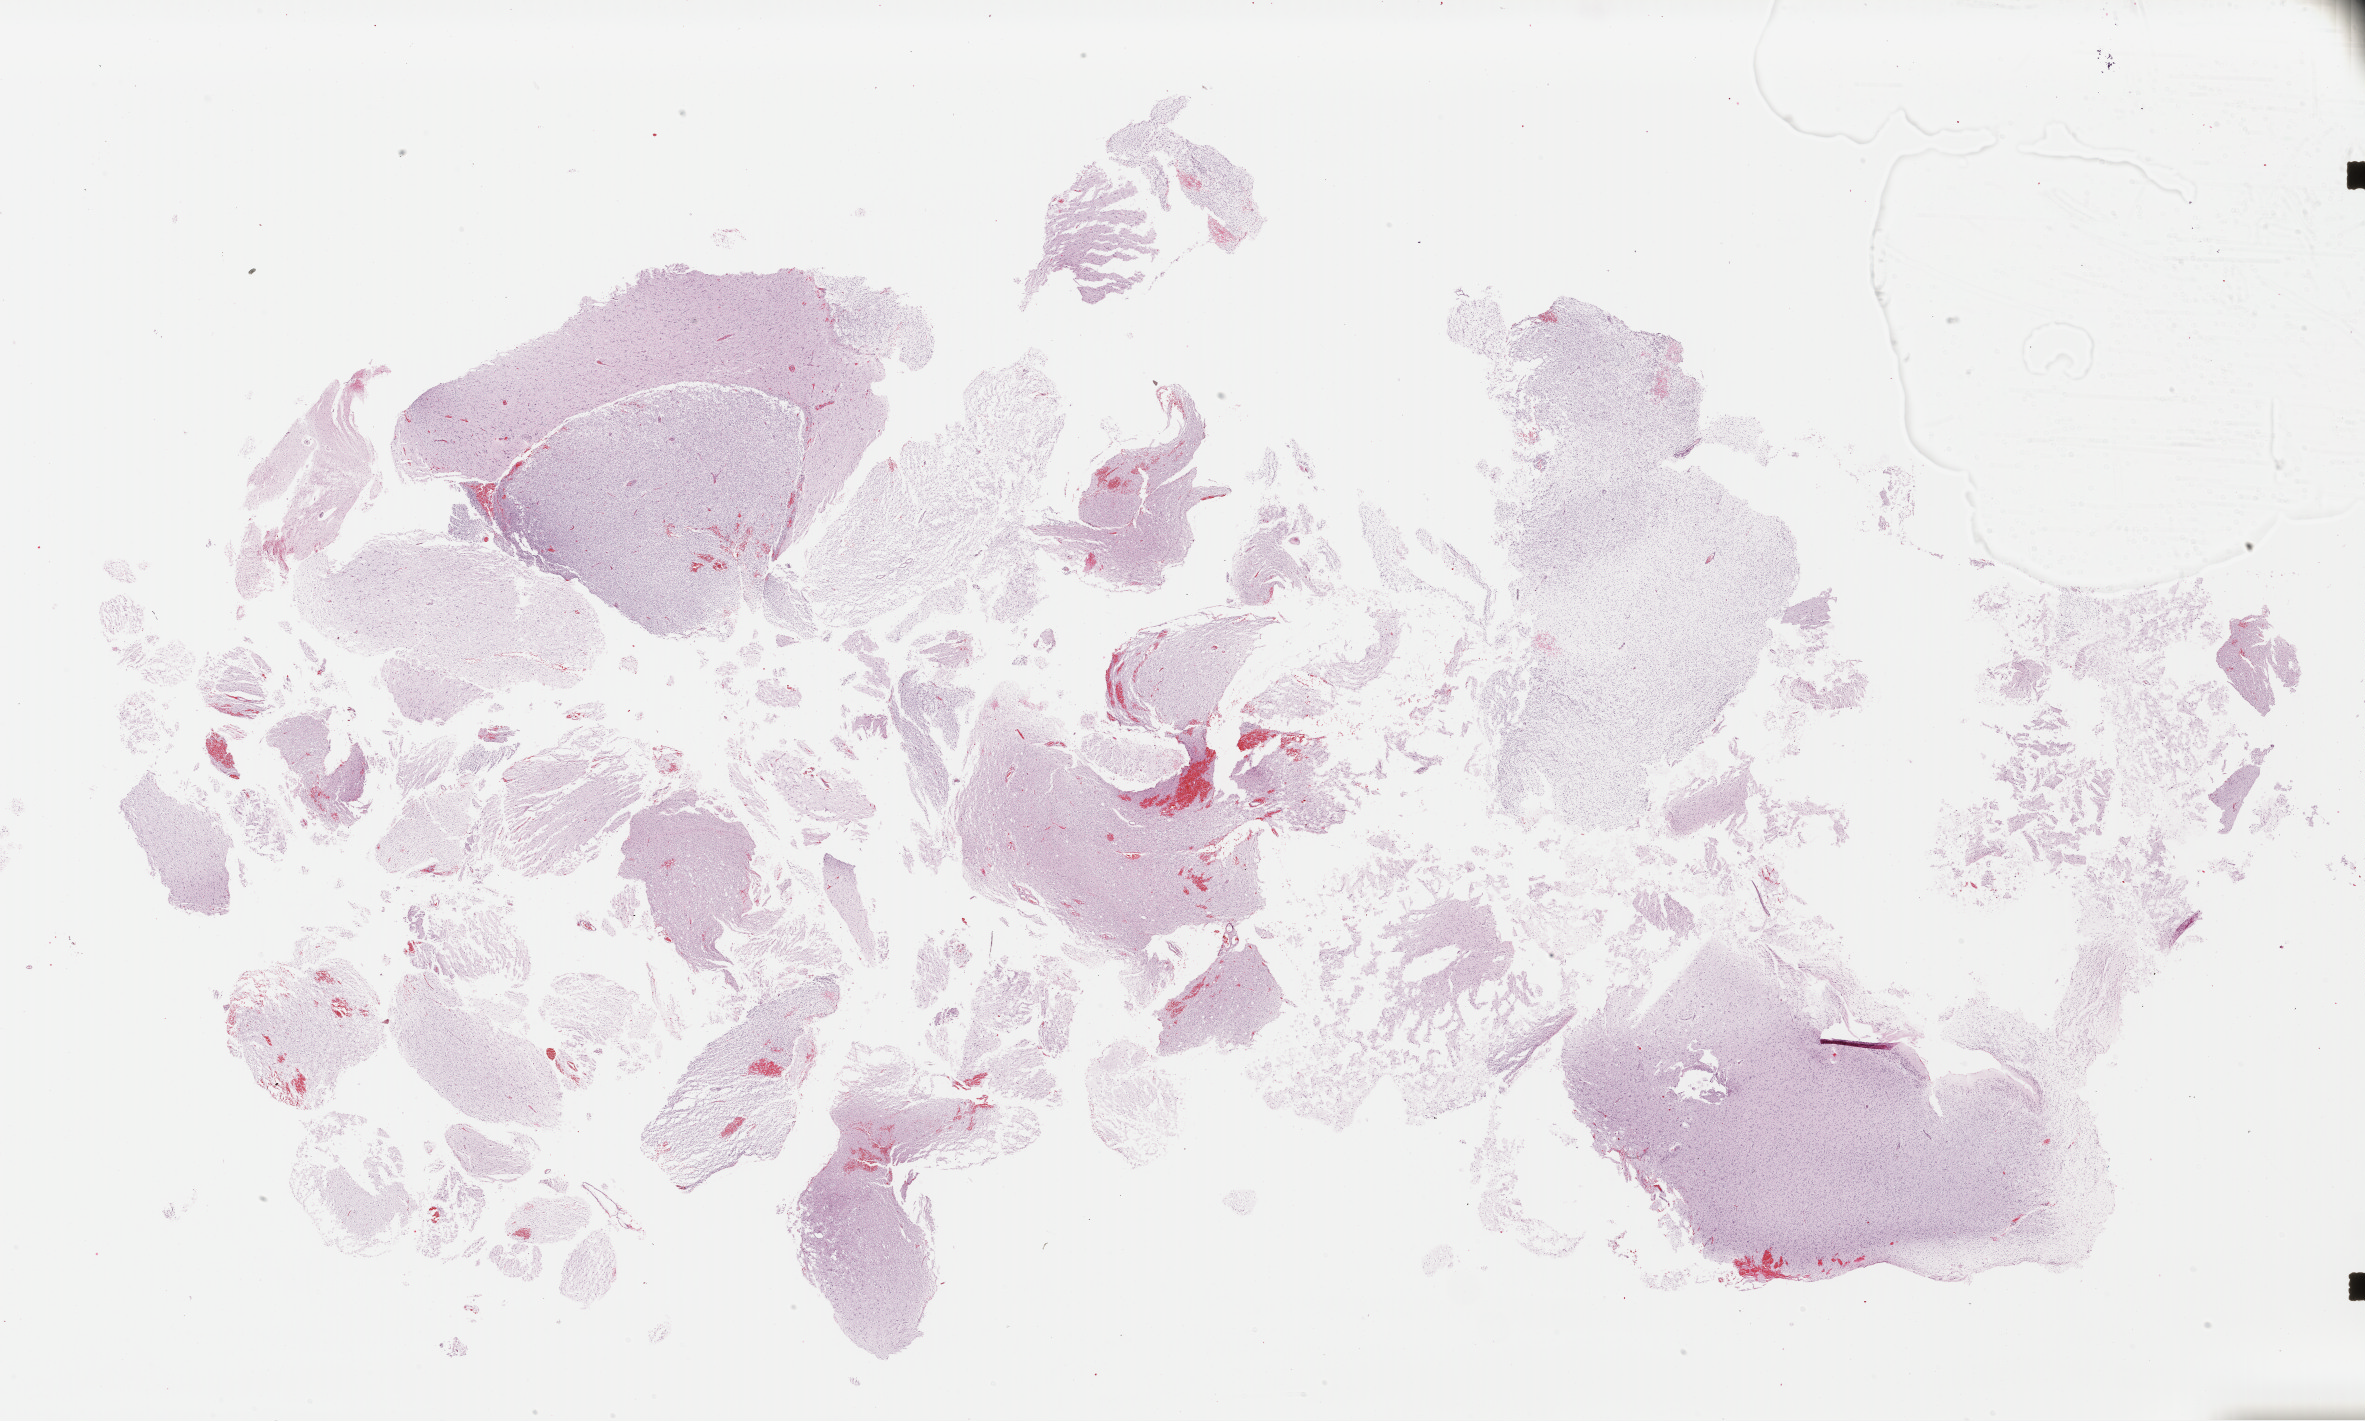
Digitized Hematoxylin and eosin (H&E) stained tissue section (whole slide) — shown as a low-resolution overview of the whole scanned area (about 37.2 x 22.3 mm, slide scanned at 40x), formalin-fixed paraffin-embedded (FFPE) diagnostic section, brain, primary tumour sample. Patient: male, age at initial diagnosis 39 years.
Pathologic diagnosis: Oligodendroglioma, NOS (cerebrum).